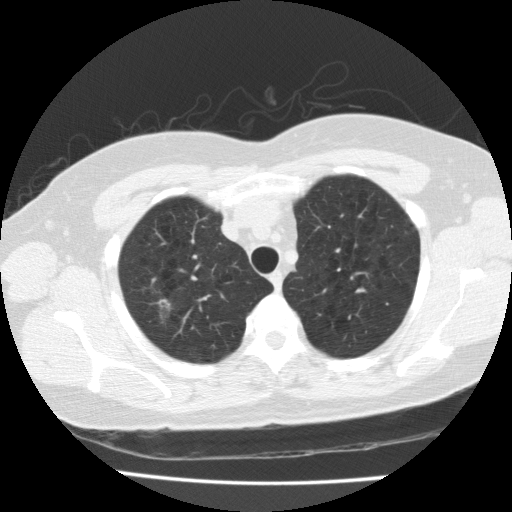
Low-dose screening chest CT, one axial slice. Slice 144 of 175 in the series (ordered by position). 120 kVp. Lung window (W 1500 / L -600 HU). 2 mm slice thickness. 512 × 512 image matrix.
Outlined on this slice (expert manual segmentation):
- lesion 1 (tumor, upper lobe of right lung): box from (x=158, y=299) to (x=170, y=308) px